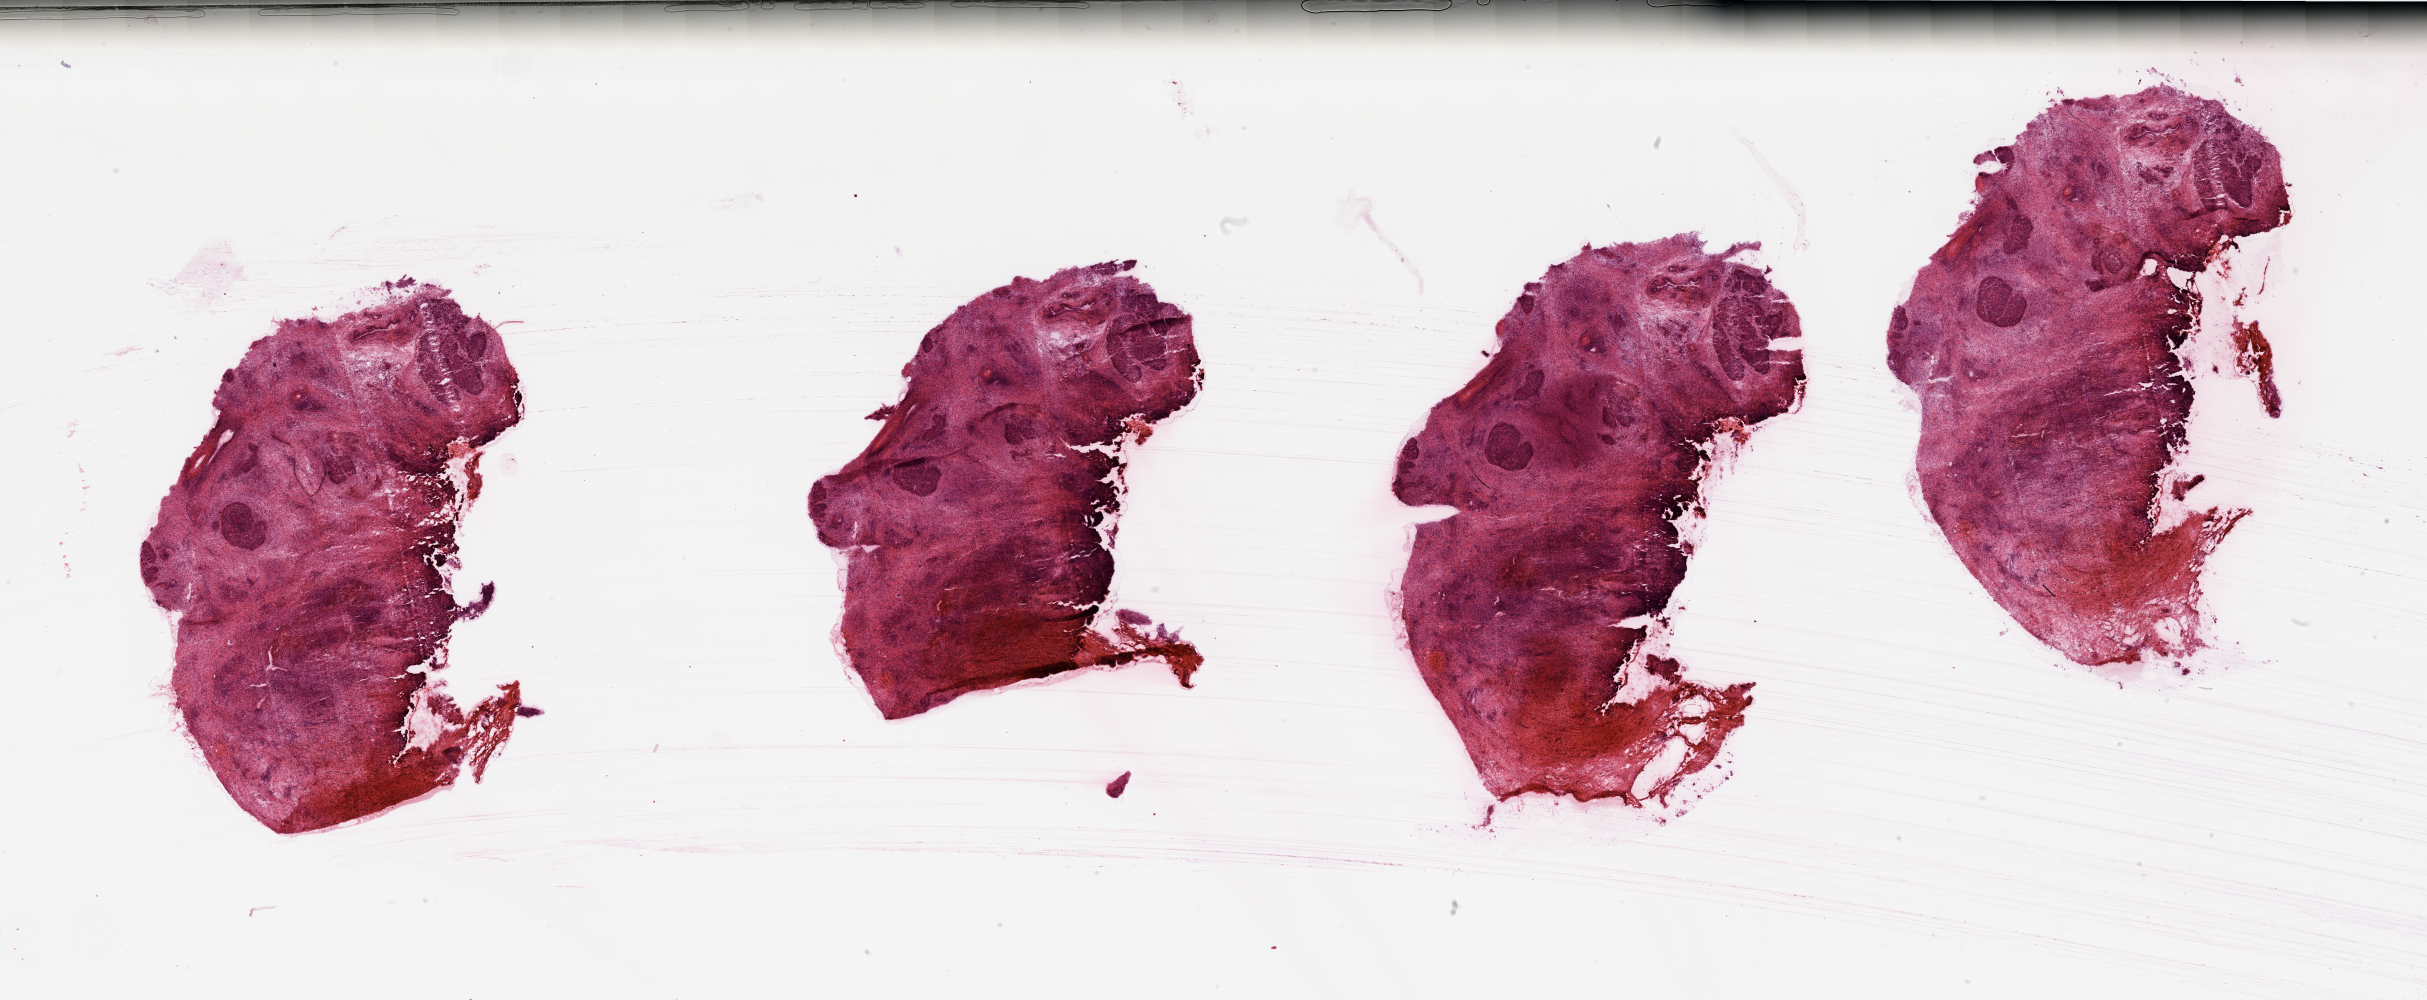
H&E whole-slide image, shown as a low-resolution overview of the whole scanned area (about 38.4 x 15.8 mm). Pancreas, normal (non-tumour) tissue. Male, 58 y/o.
This section: normal (non-tumour) tissue from the same patient. Patient diagnosis: Infiltrating duct carcinoma, NOS.